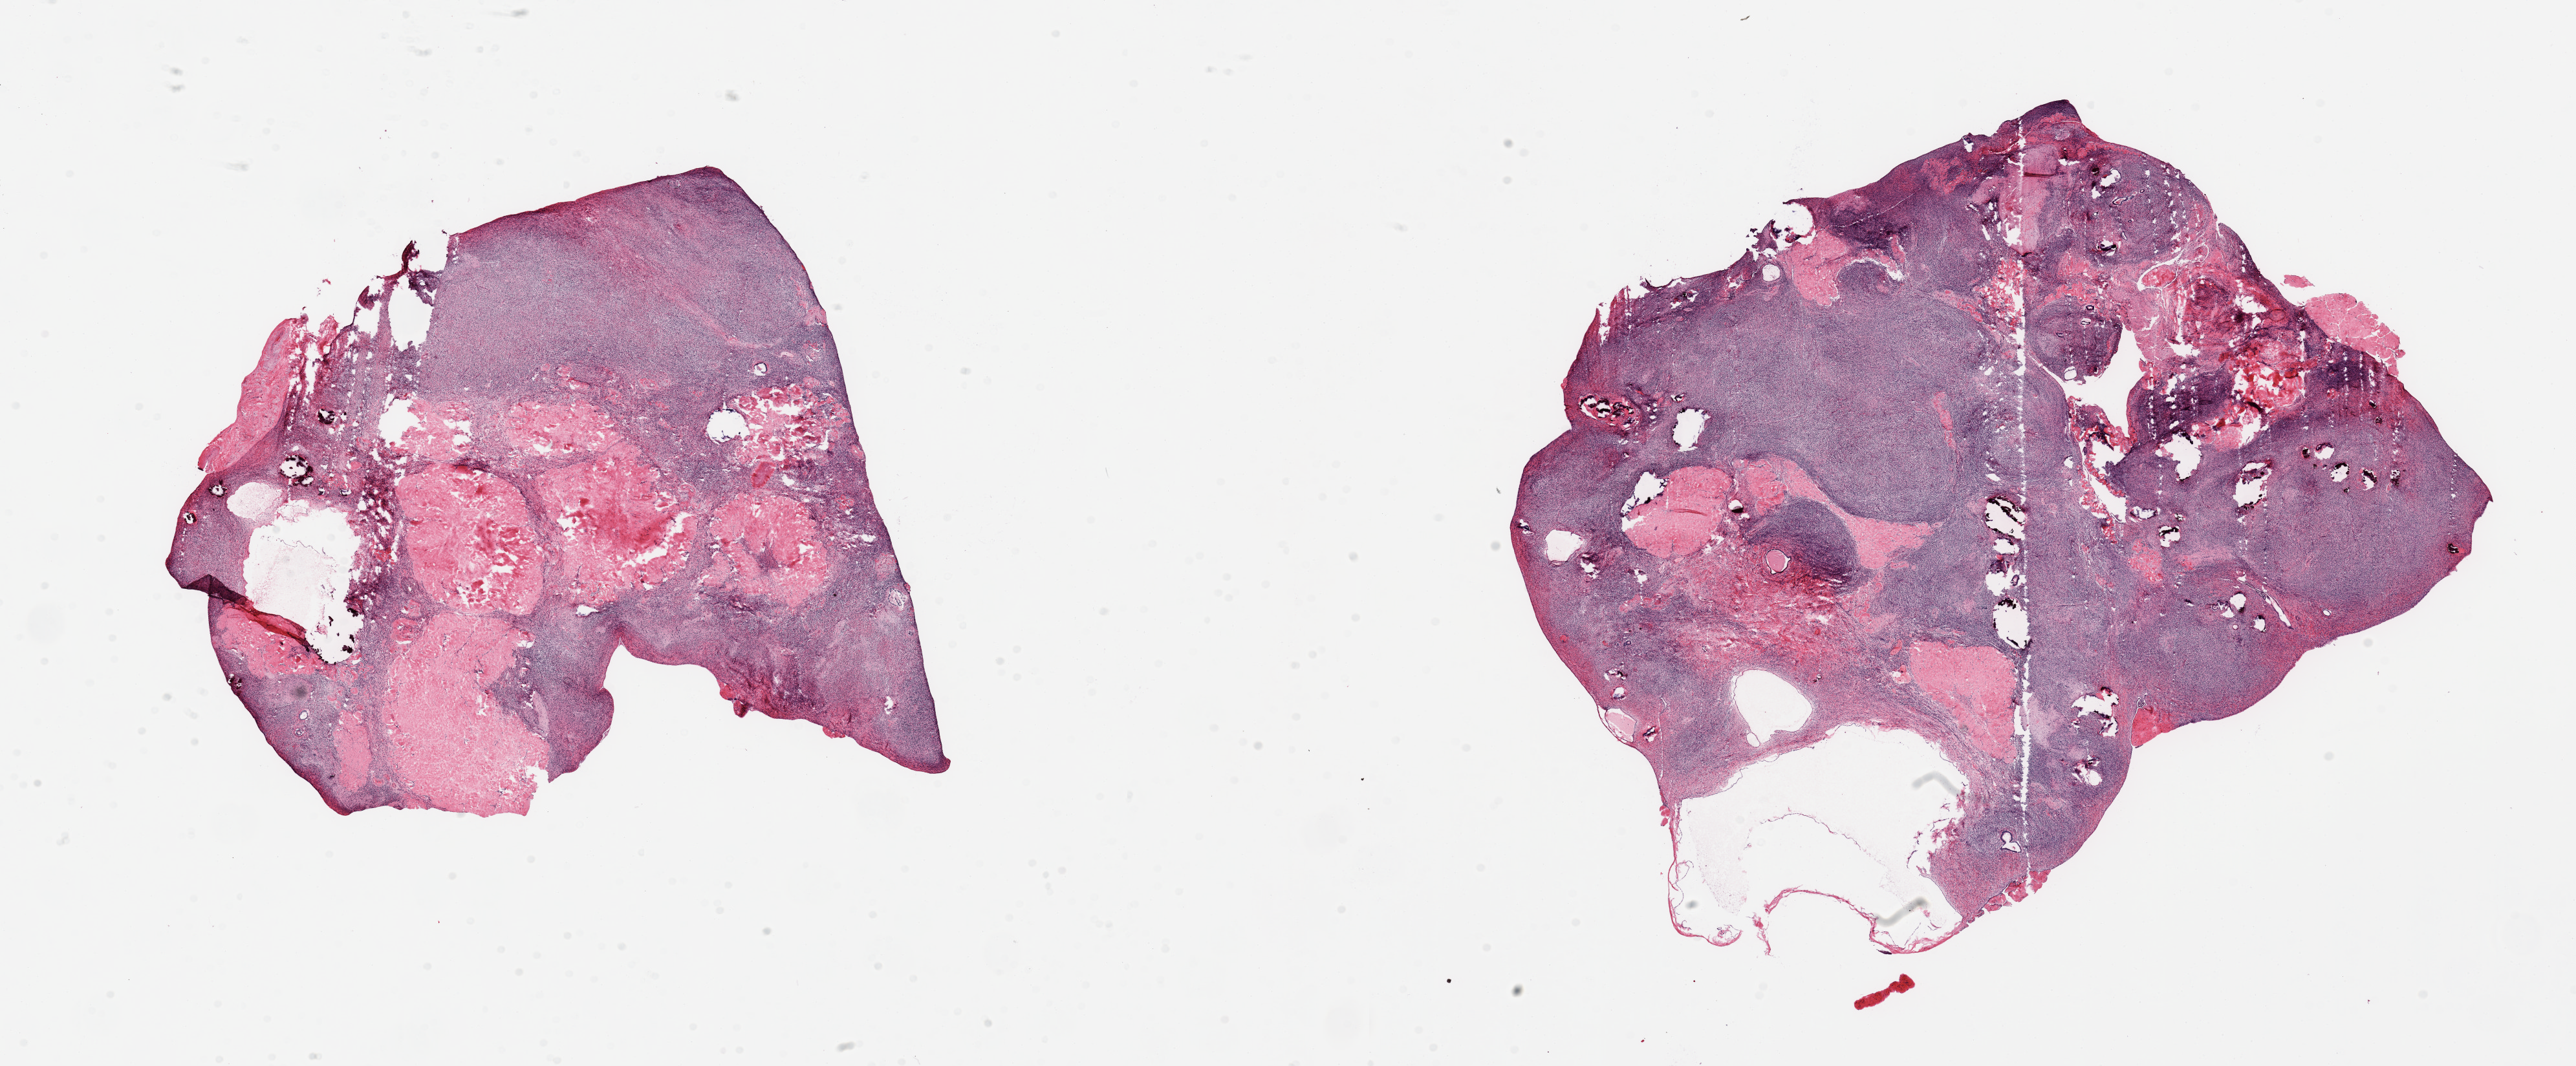
H&E whole-slide image — whole scanned area (about 31.5 x 13.0 mm, slide scanned at 20x) shown as a low-resolution overview. PAXgene-fixed, paraffin-embedded tissue. Sampled site (target tissue): ovary. Tissue donor sample. Donor: female.
Pathologist's review note for this sample: 2 pieces, post menopausal atrophy.